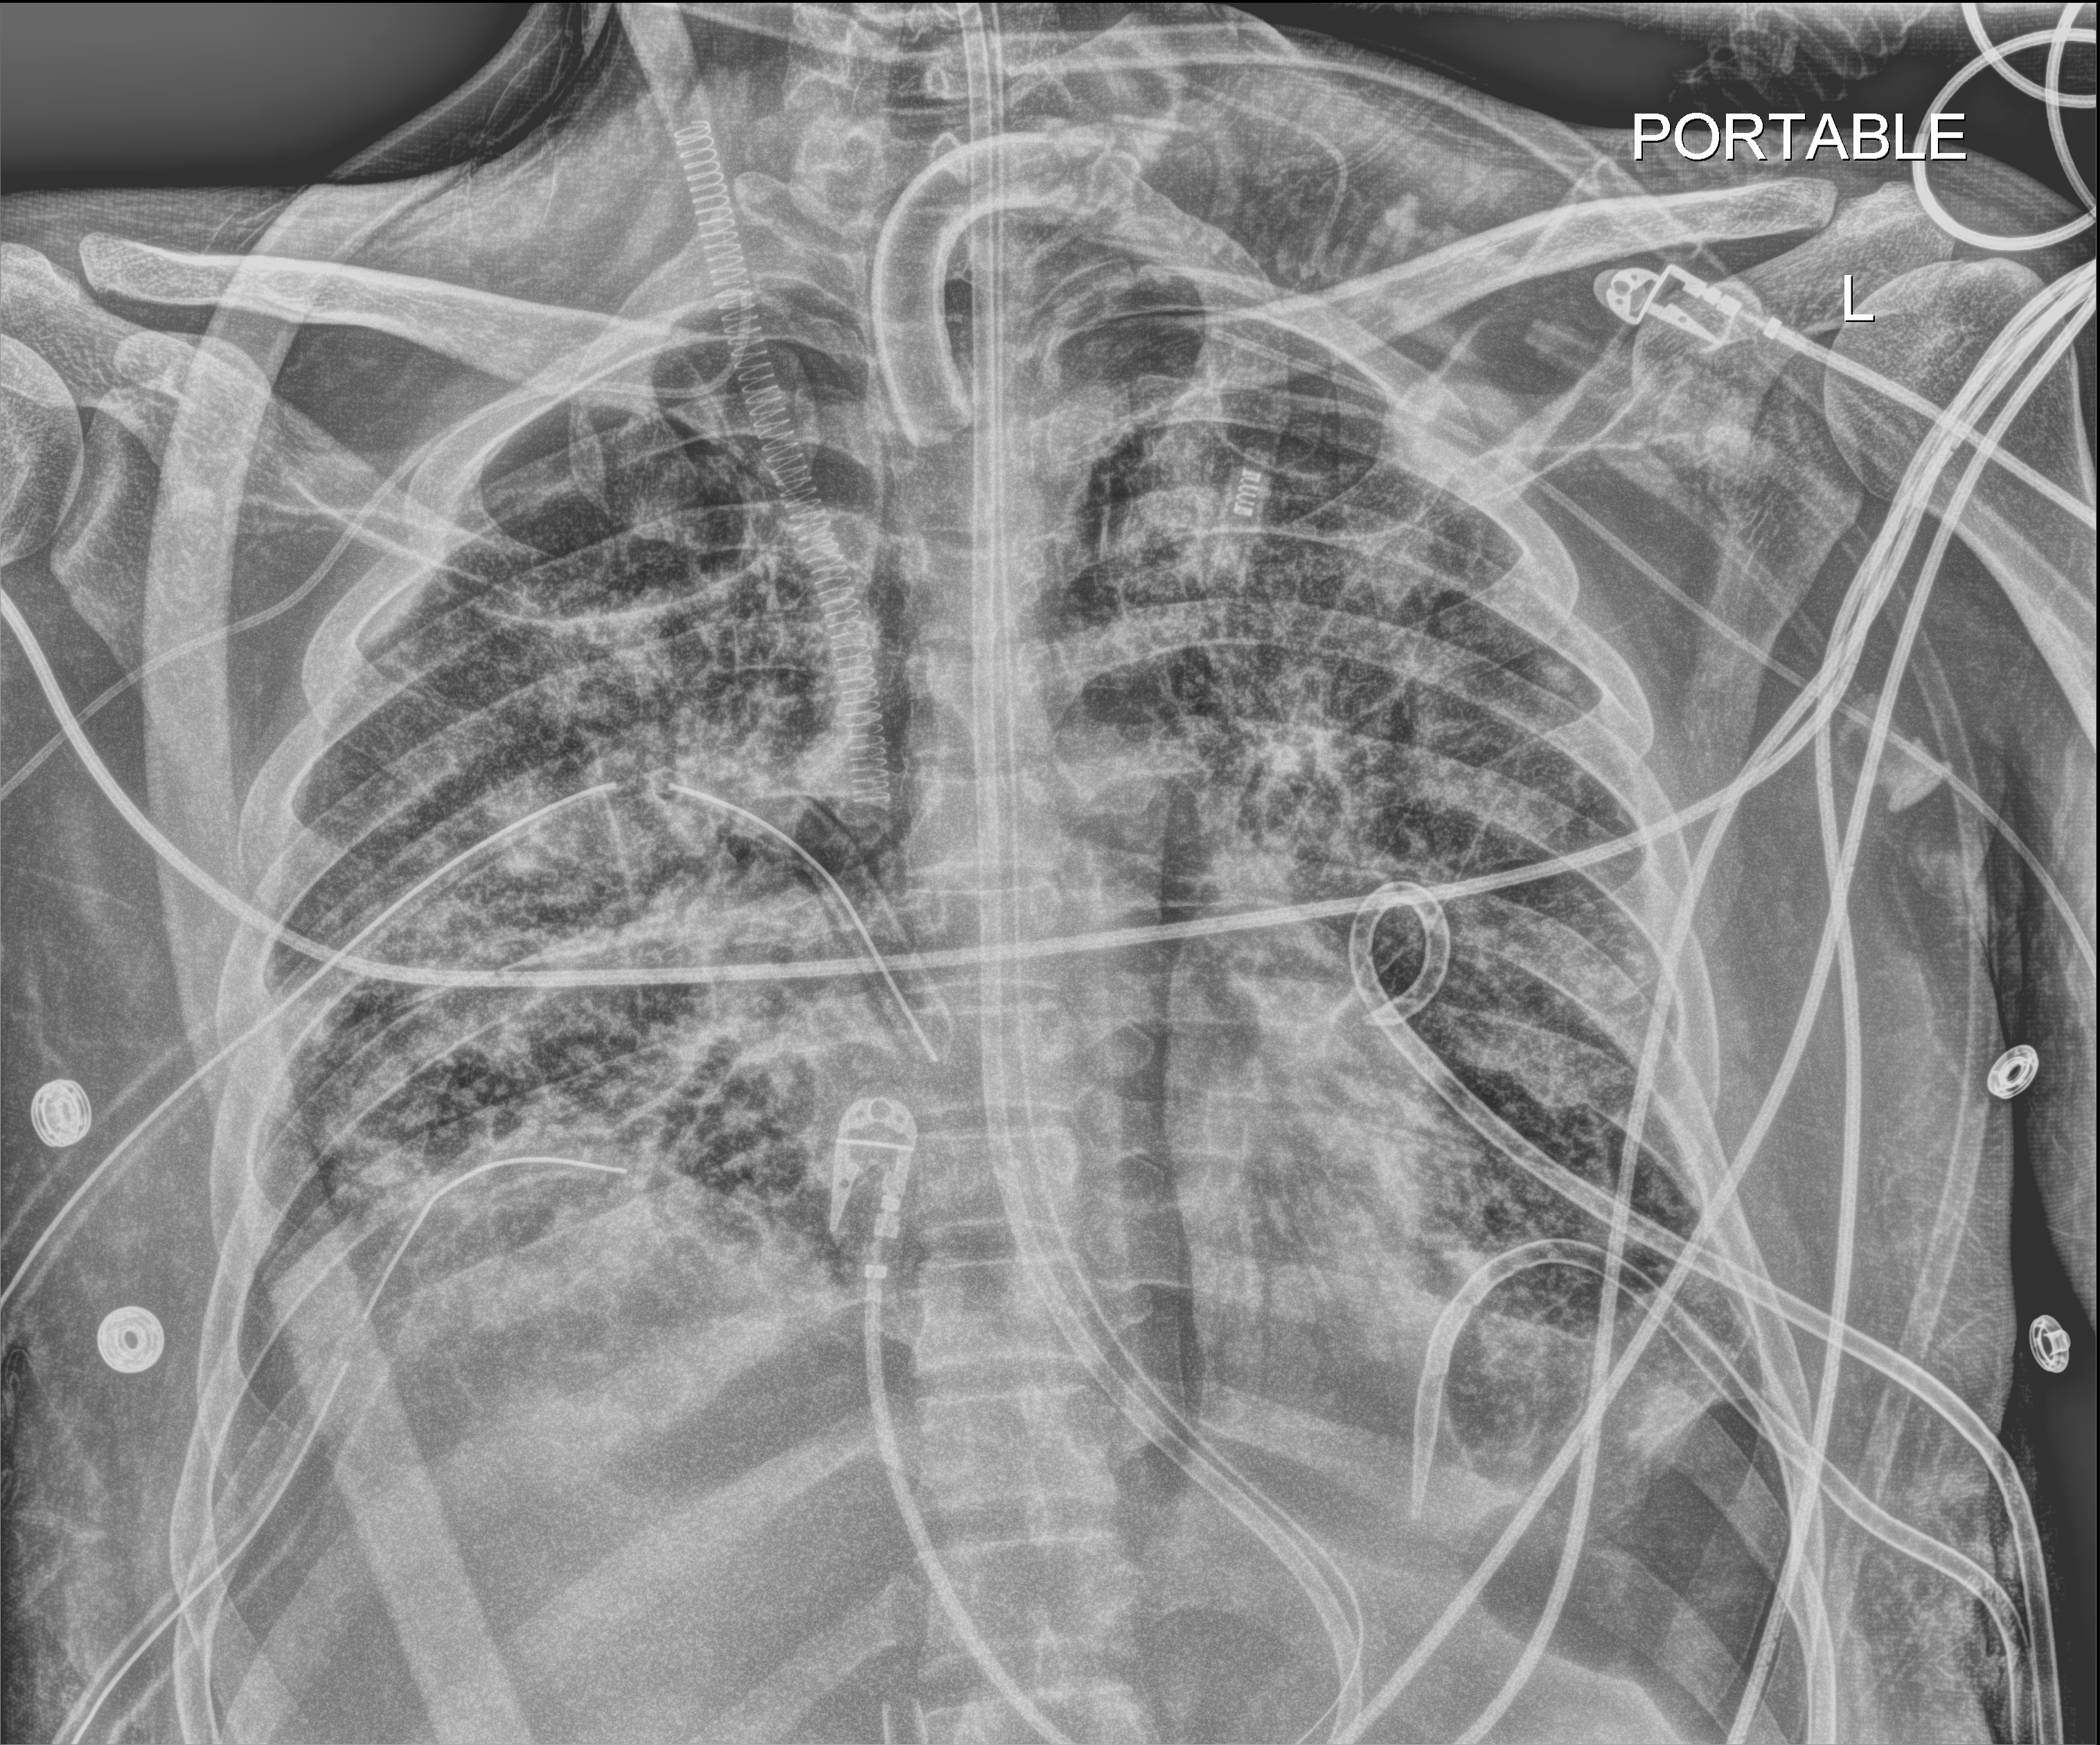
Portable chest radiograph; anteroposterior (AP) projection. Adult patient hospitalised with COVID-19, age 18–59 years.
Admission-level facts for this patient (not findings on this image; timing relative to this image not recorded): length of hospital stay: 60 days; other chronic lung disease (admission record): no.